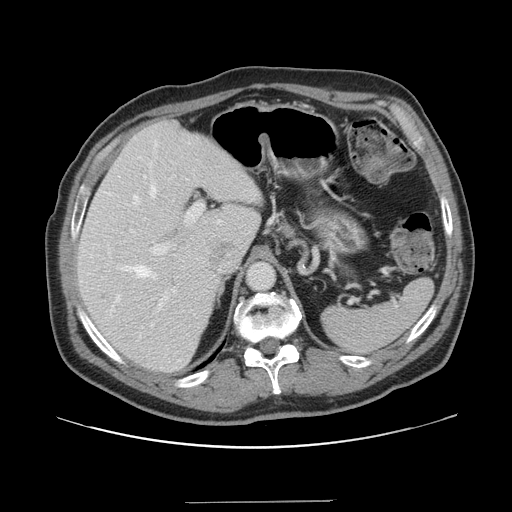
Contrast-enhanced abdominal CT, one axial slice. 120 kVp. Soft-tissue window (W 400 / L 40 HU). 2.5 mm slice thickness. 512 × 512 image matrix, field of view 399 × 399 mm. Male patient, age 63 years. Case-level facts recorded for this patient, not image findings: diagnosis: colorectal cancer liver metastases, imaged before liver resection; multiple liver metastases: no; largest metastasis: 2.1 cm; chemotherapy before resection: no.
Structures marked on this image (expert manual segmentation):
- hepatic veins: bounding box (x1, y1, x2, y2) in pixels: (117, 143, 157, 301)
- liver: (78, 121, 263, 373)
- planned liver remnant (the part of the liver to remain after resection): (78, 121, 260, 373)
- portal vein (with intrahepatic branches): (150, 203, 204, 311)